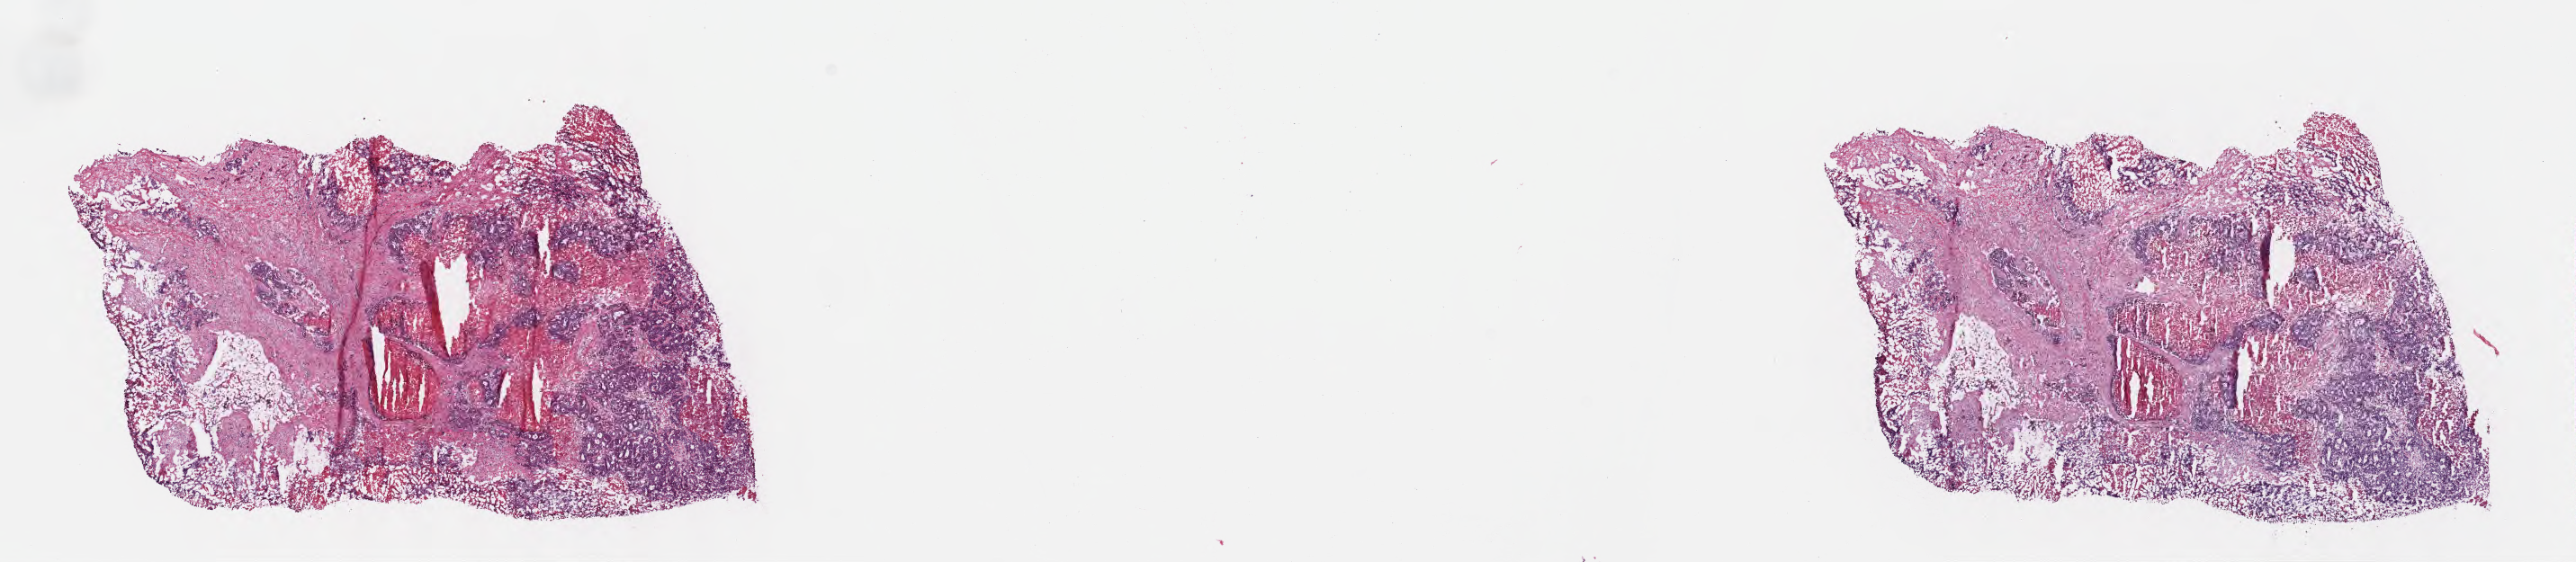
Whole-slide image, haematoxylin and eosin stain — whole scanned area (about 23.1 x 5.1 mm) shown as a low-resolution overview; frozen section (tissue freezing medium); specimen: metastatic tumor tissue, resected from liver. Female patient; age at initial diagnosis 58 years.
Patient diagnosis (primary): Adenocarcinoma, NOS.